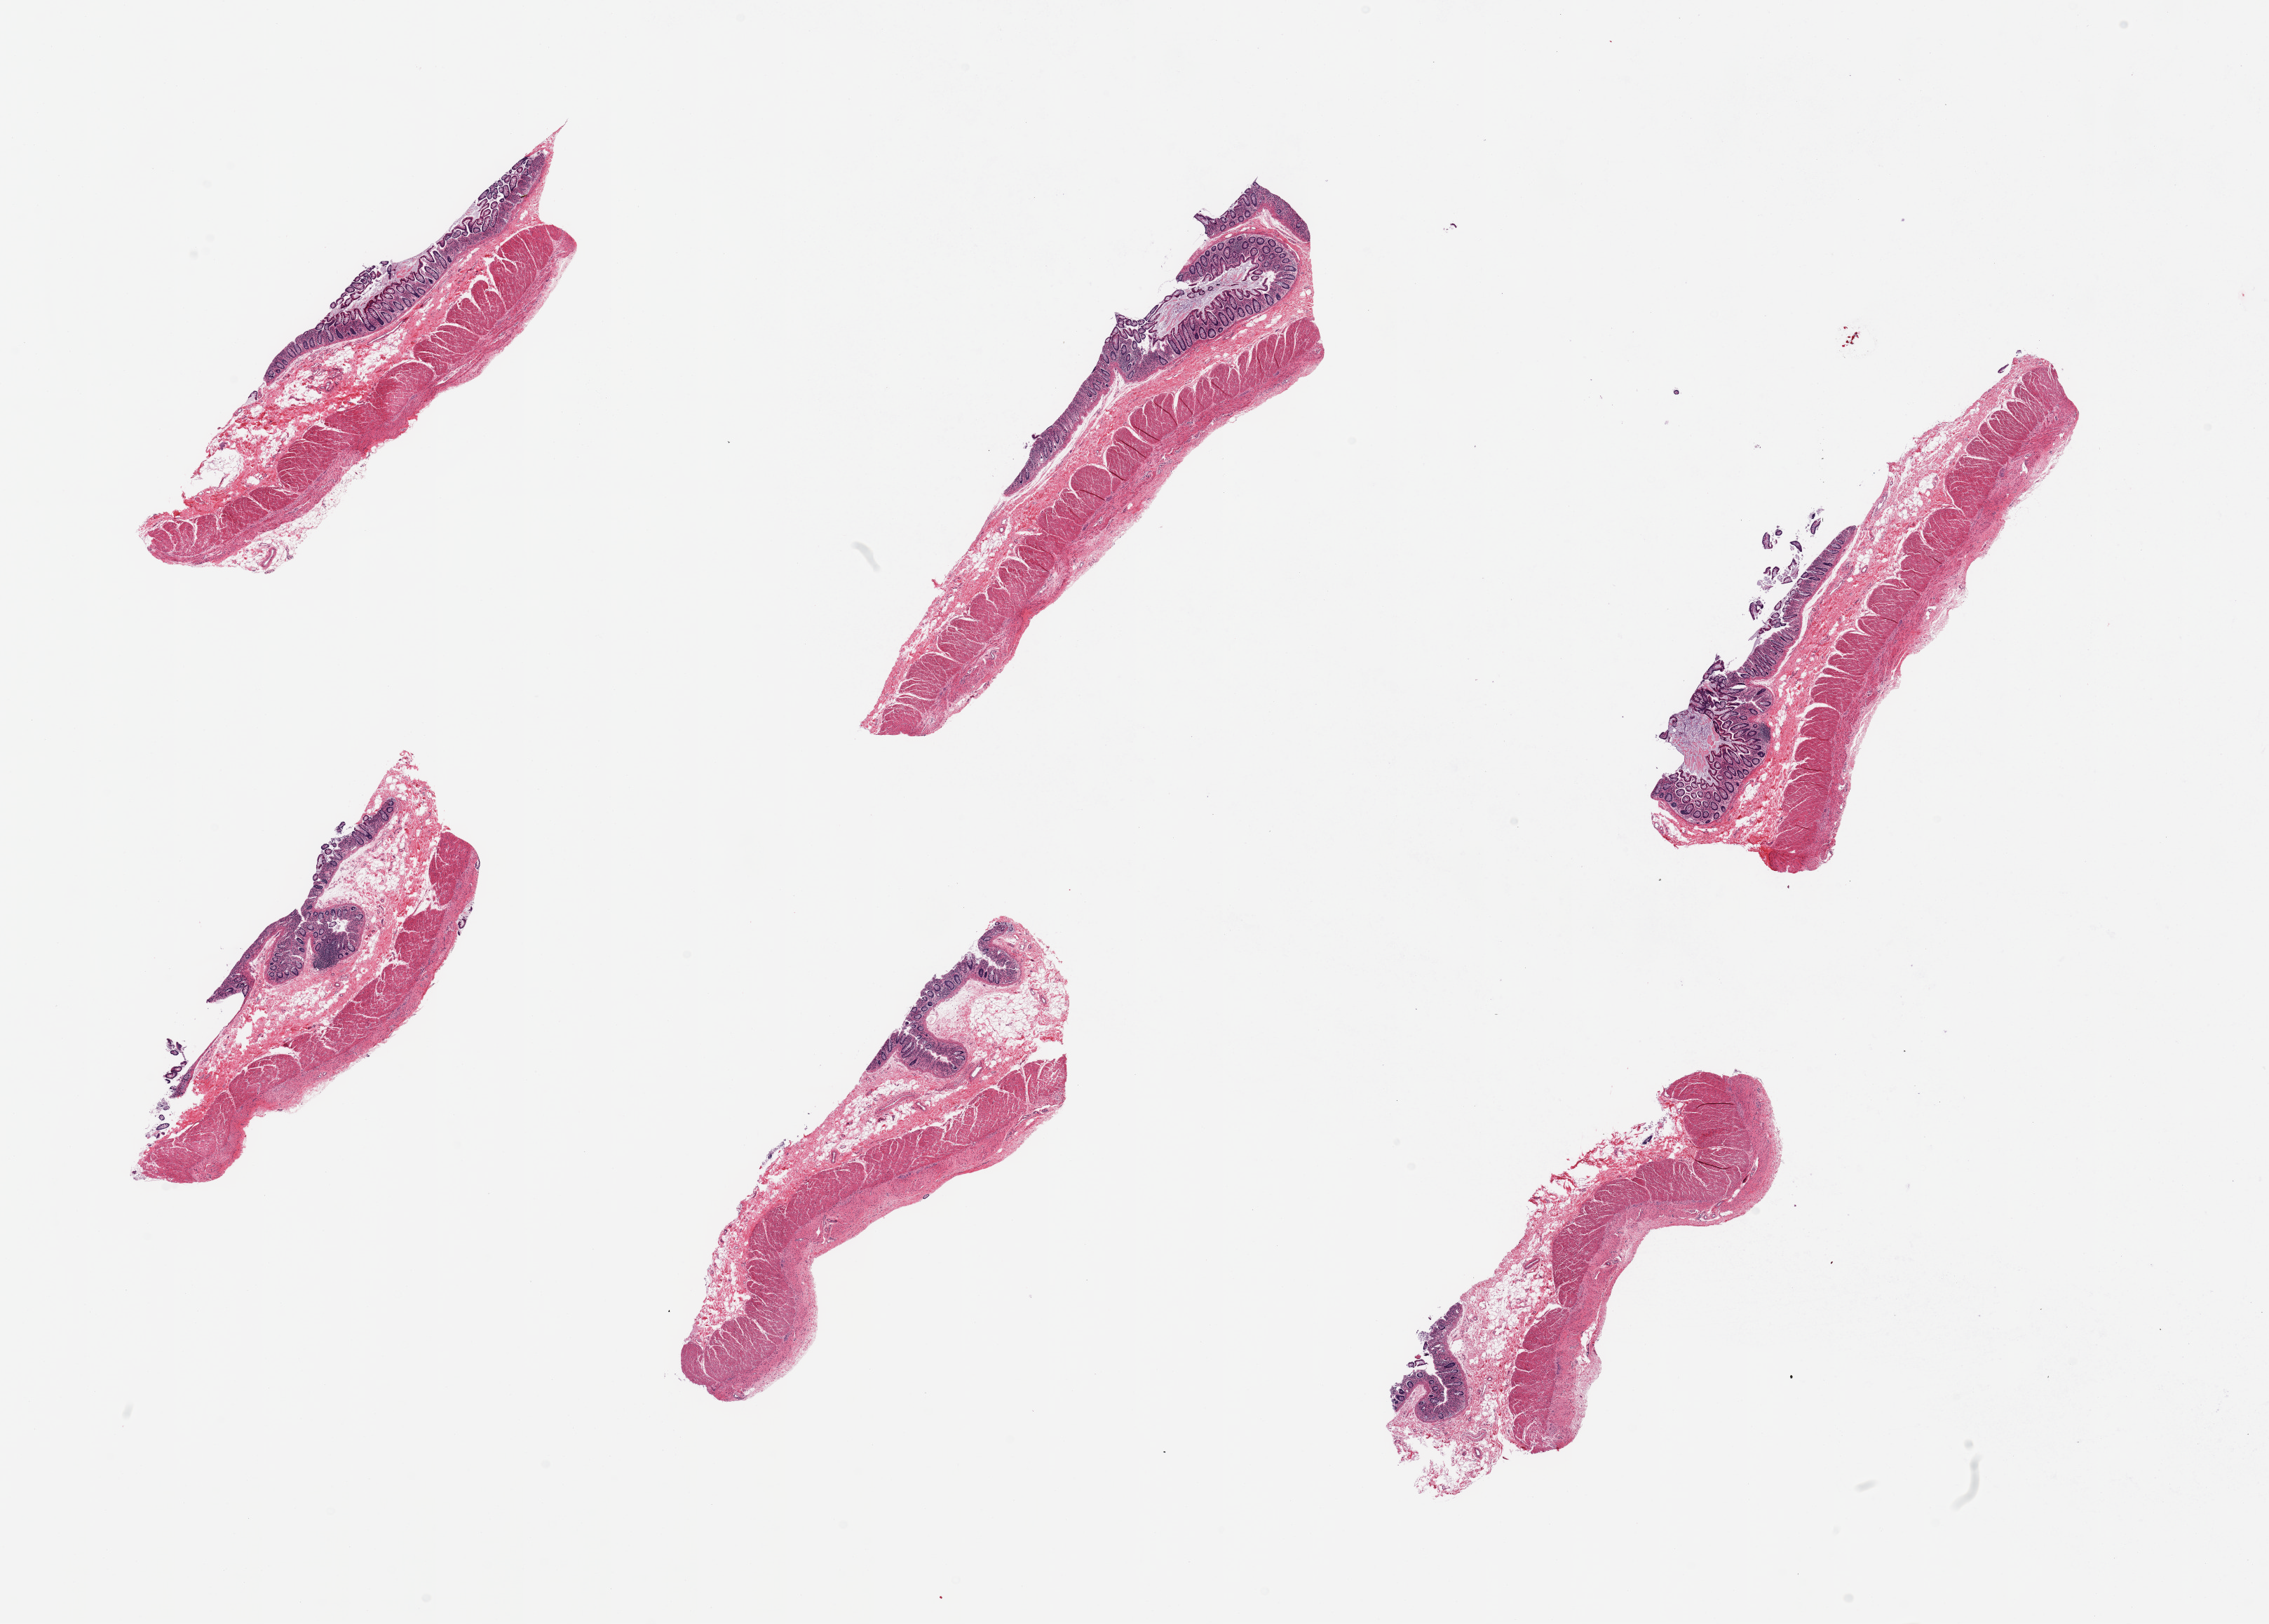
Digitized hematoxylin and eosin (H&E)-stained section, shown as a low-resolution overview of the whole scanned area (about 25.6 x 18.3 mm), PAXgene-fixed paraffin-embedded (PFPE) section, section of transverse colon (target tissue), tissue donor sample.
Pathologist's review note for this sample: 6 pieces; epithelial autolysis varies from 1 to 2.